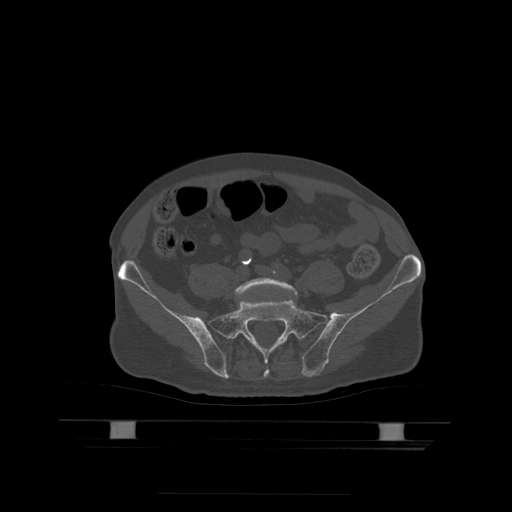
CT including the spine, one axial slice; position 57 of 522 along the scan axis; bone window (W 1800 / L 400 HU); 1.25 mm slice thickness; 512 × 512 image matrix, field of view 436 × 436 mm. Patient age 68 years. From the clinical record (not read from this slice): primary cancer: urothelial.
Structures marked on this image (semi-automatic segmentation, software-assisted and operator-edited):
- L5 vertebra: bounding box (x1, y1, x2, y2) in pixels: (235, 278, 298, 297)